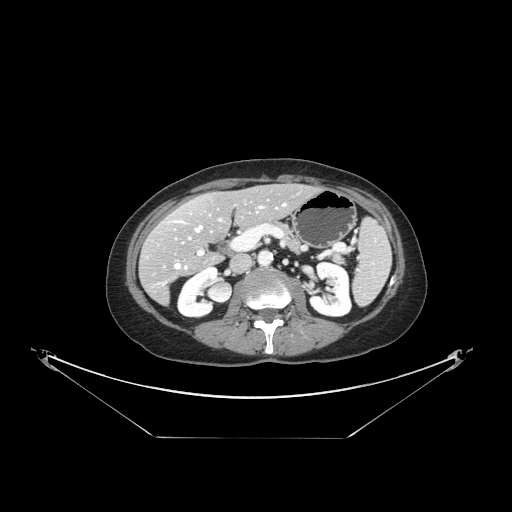
Contrast-enhanced abdominal CT, one axial slice; position 71 of 148 along the scan axis; intravenous contrast given; soft-tissue window (W 400 / L 40 HU); 512 × 512 image matrix, field of view 500 × 500 mm. Female patient, age 73 years. From the clinical record (not read from this slice): diagnosis: colorectal cancer liver metastases, imaged before liver resection.
Outlined on this slice (expert manual segmentation):
- hepatic veins: bounding box <162,204,285,285> (left, top, right, bottom; pixels)
- liver: <140,186,315,302>
- planned liver remnant (the part of the liver to remain after resection): <168,186,315,247>
- portal vein (with intrahepatic branches): <198,206,263,256>